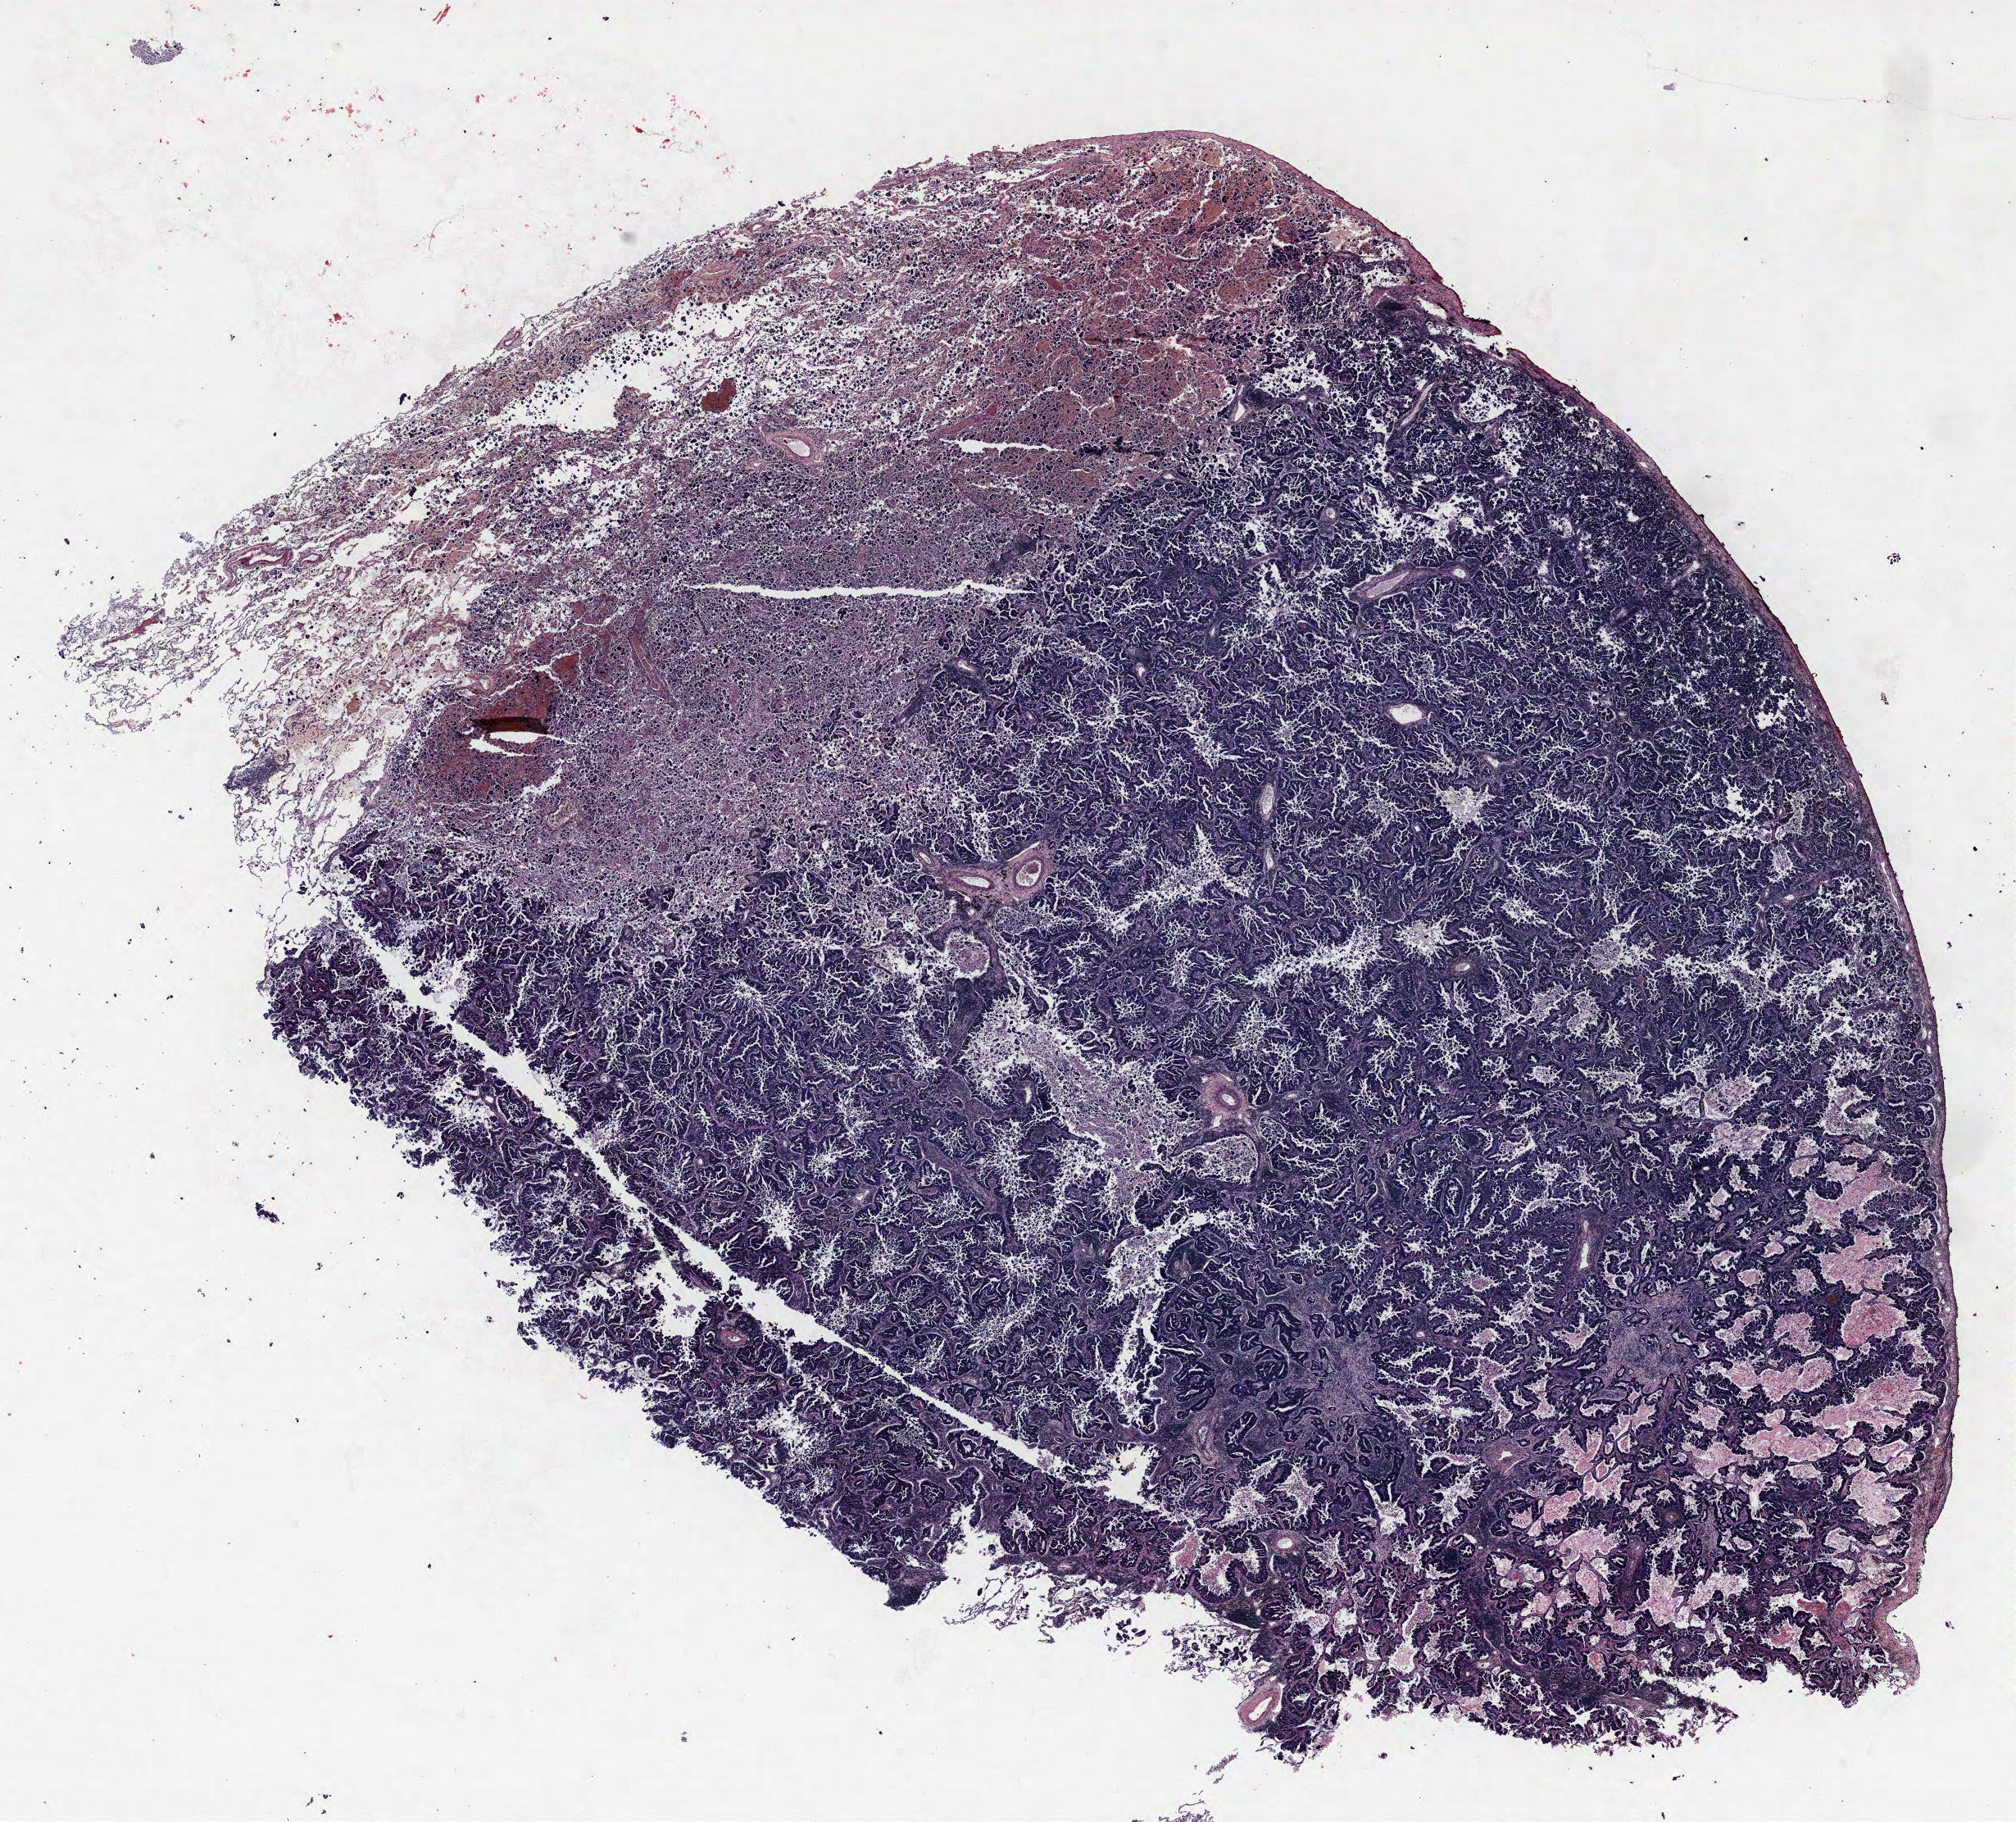
Whole-slide histology image, H&E — a low-resolution overview of the entire scanned area, about 19.7 x 17.8 mm (slide scanned at 40x), FFPE section, lung tissue. Male patient, aged 69 at enrolment. Former smoker at enrolment. Grade: moderately differentiated (G2).
Participant's lung-cancer diagnosis: Adenocarcinoma, NOS. ICD-O-3 topography: upper lobe of lung (C34.1). Stage (AJCC 6th edition): IA. Tumour size (pathology): 23 mm. Primary tumour location (clinical record): right upper lobe.